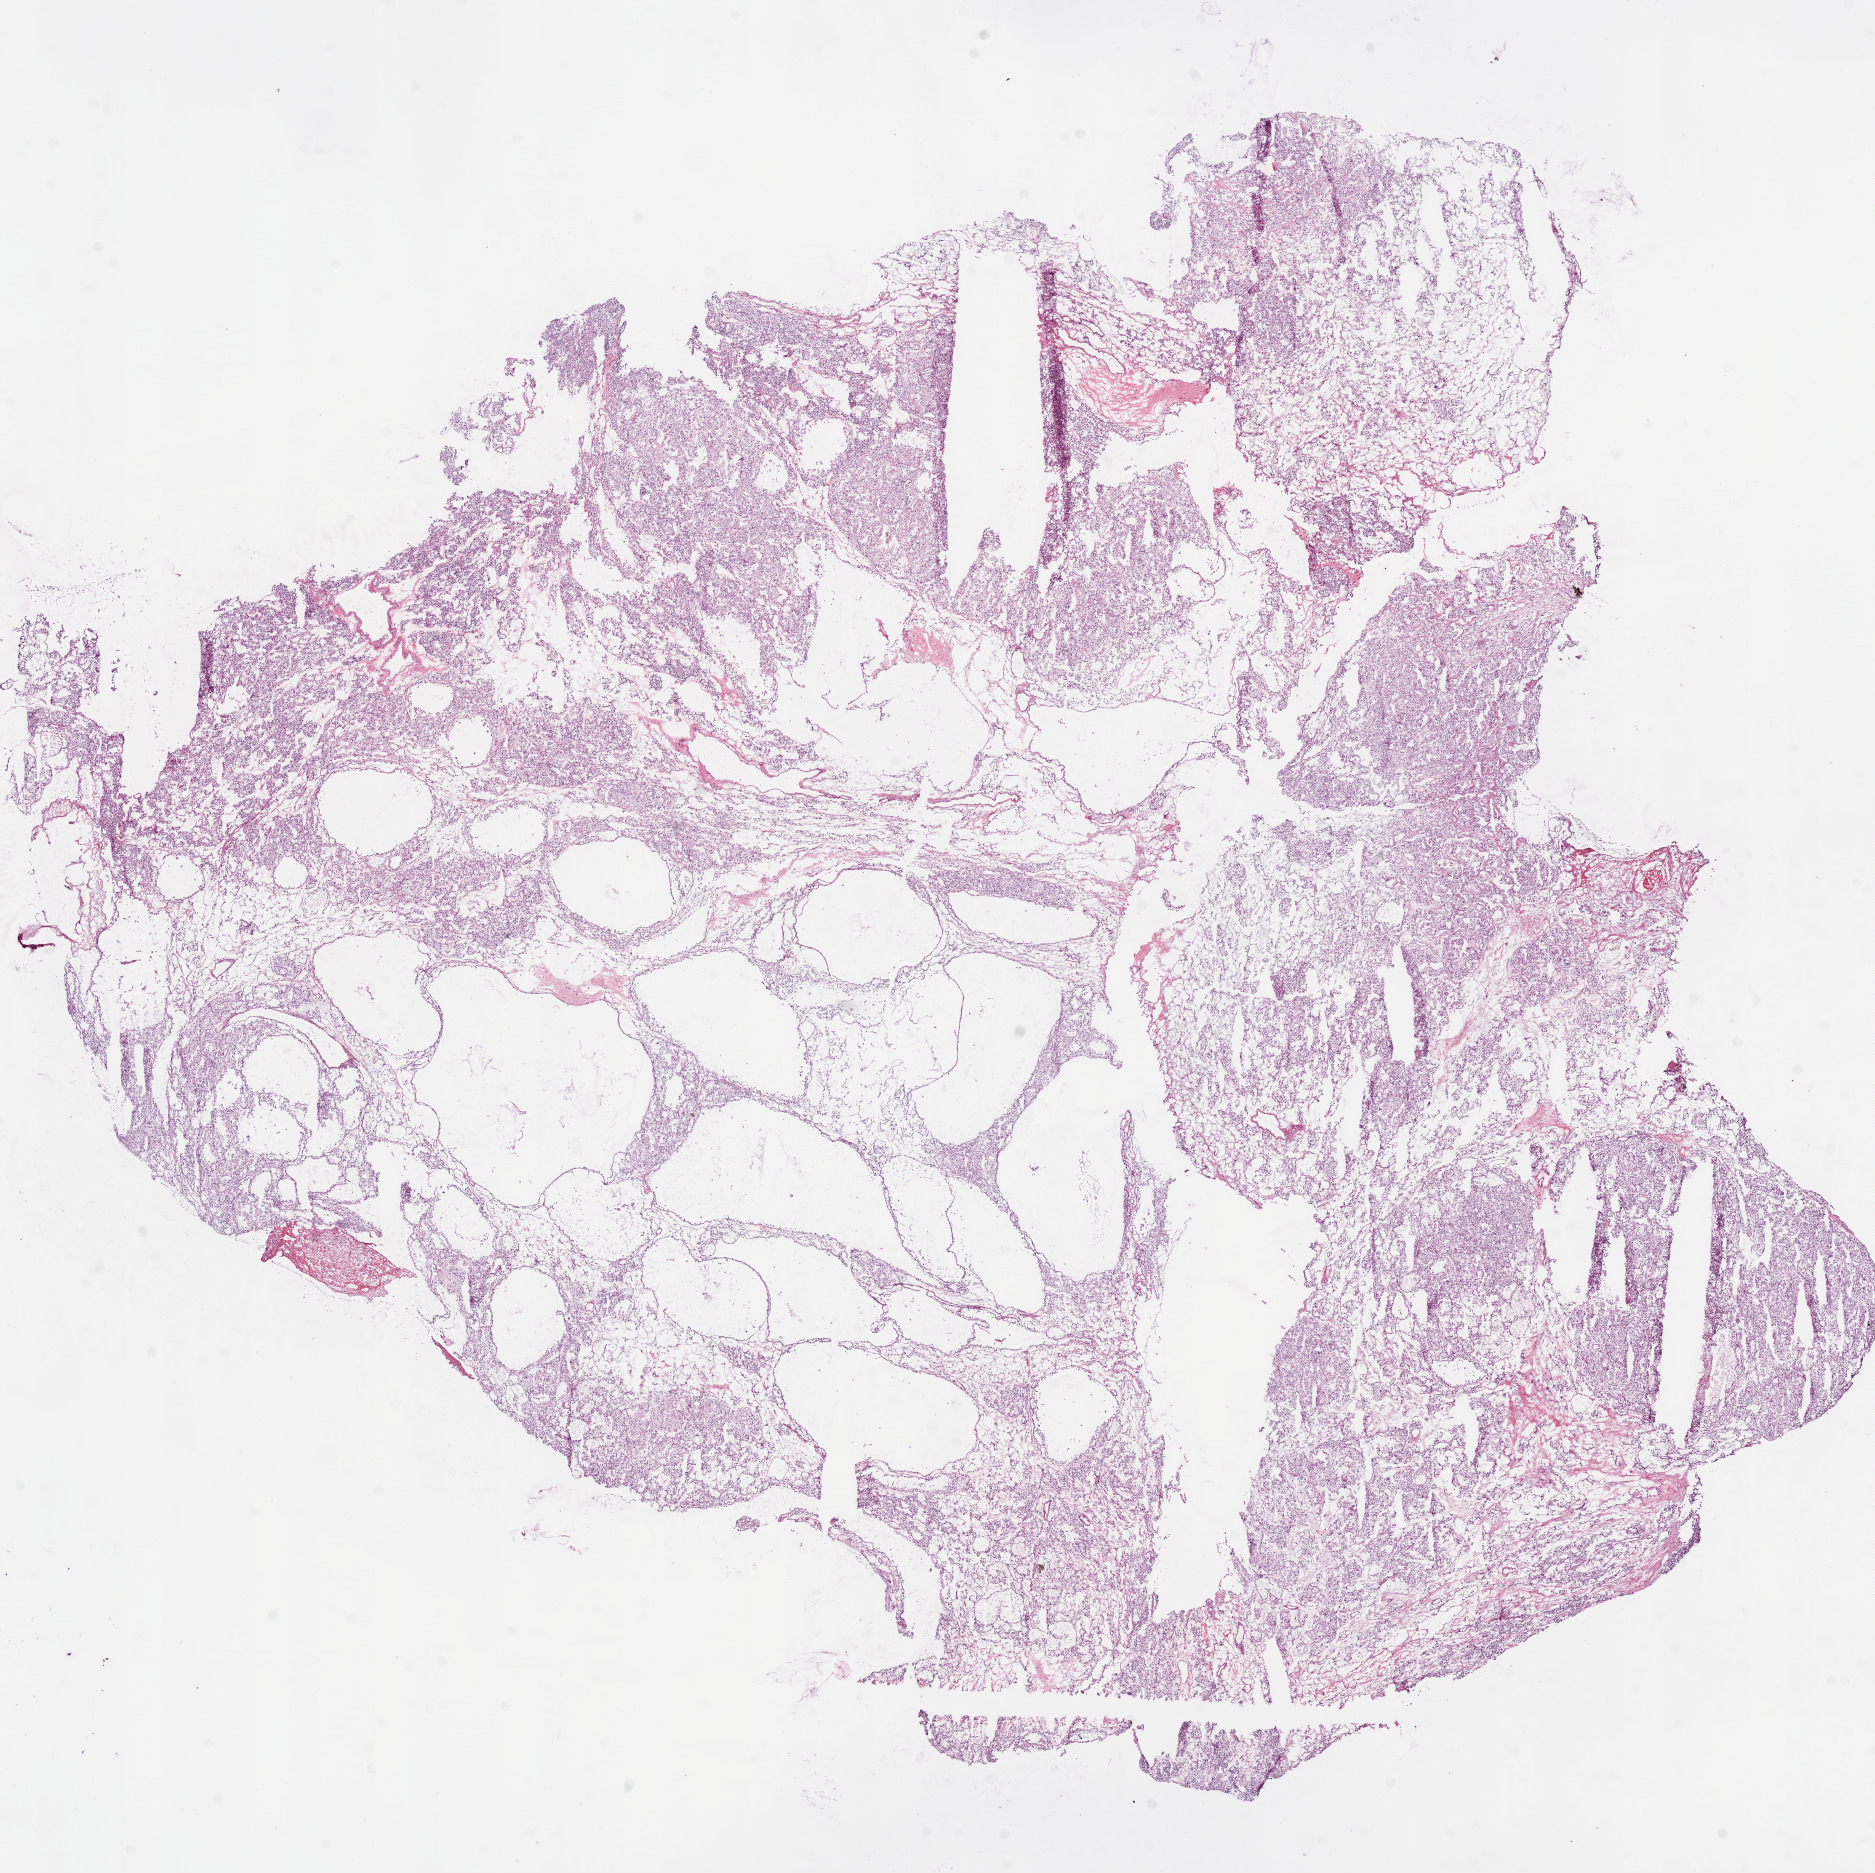
Whole-slide histology image, Hematoxylin and eosin (H&E) stained, low-resolution overview of the scanned area, about 15.0 x 15.0 mm (from a 20x scan), frozen section, sample: primary tumour, kidney. Patient: male, age at initial diagnosis 58 years. Histologic grade: G3 (poorly differentiated). Composition of this section per pathologist review: tumour cells 85%, tumour nuclei 80%, normal cells 0%, stromal cells 15%, necrosis 0%.
• AJCC pathologic stage: I
• laterality: left
• pathologic diagnosis: Clear cell adenocarcinoma, NOS